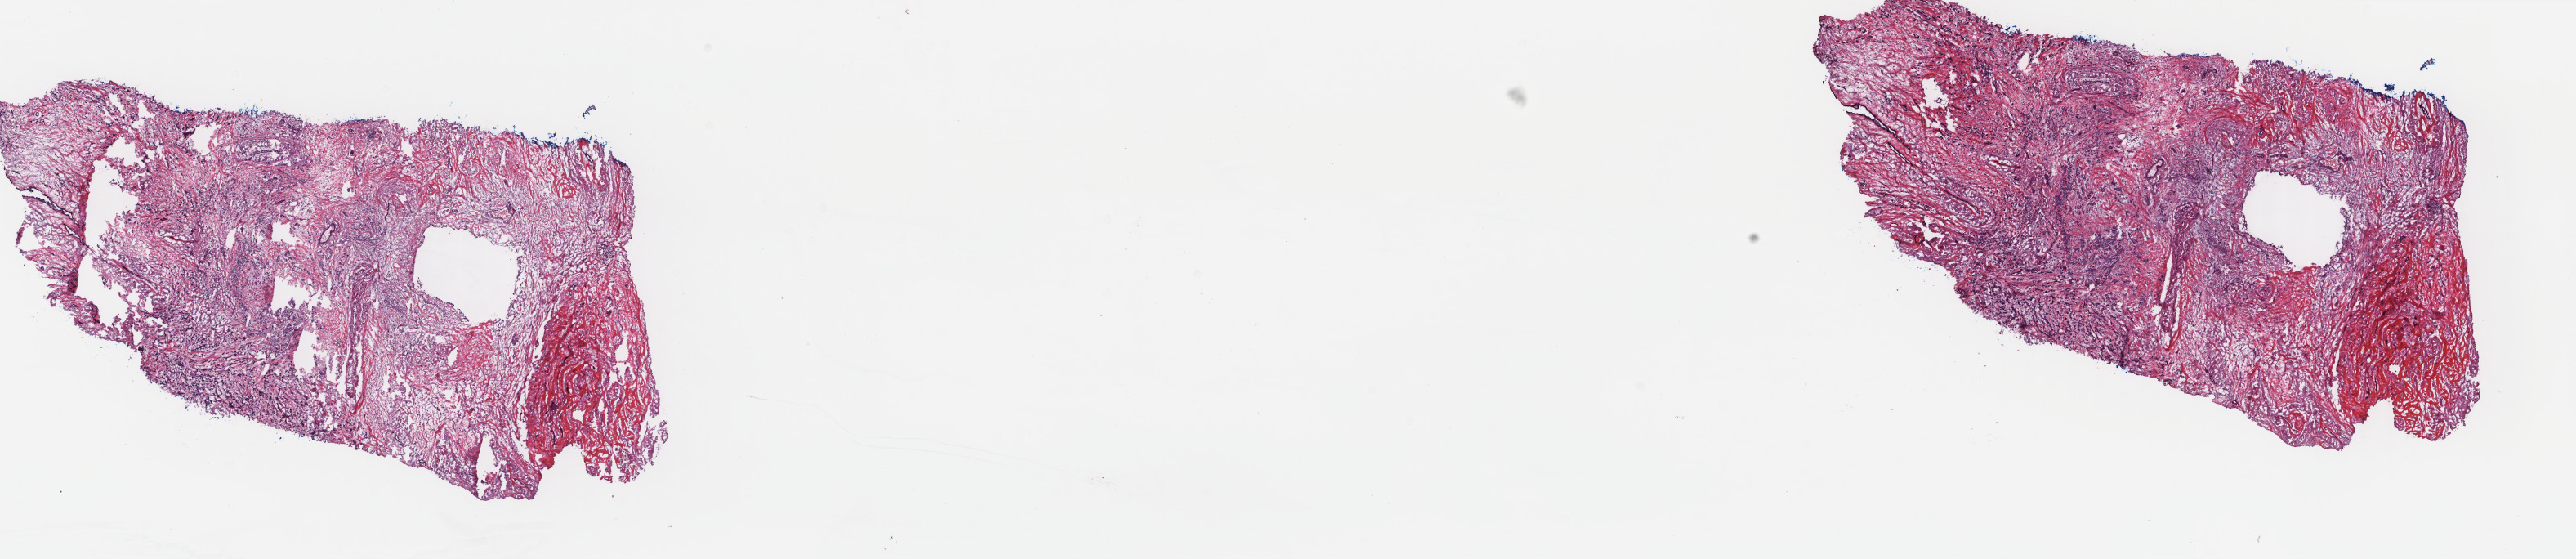
H&E-stained whole-slide image — whole scanned area (about 25.0 x 5.4 mm) shown as a low-resolution overview. Frozen section. Breast, primary tumour sample. Patient: female, age at initial diagnosis 76 years. Slide review estimates, as recorded: tumour cells 50%, tumour nuclei 65%, normal cells 10%, stromal cells 40%, necrosis 0%. Inflammatory infiltration, as recorded: lymphocyte infiltration 1%, monocyte infiltration 0%, neutrophil infiltration 0%.
- AJCC pathologic stage: IIA (6th edition)
- pathologic diagnosis: Lobular carcinoma, NOS